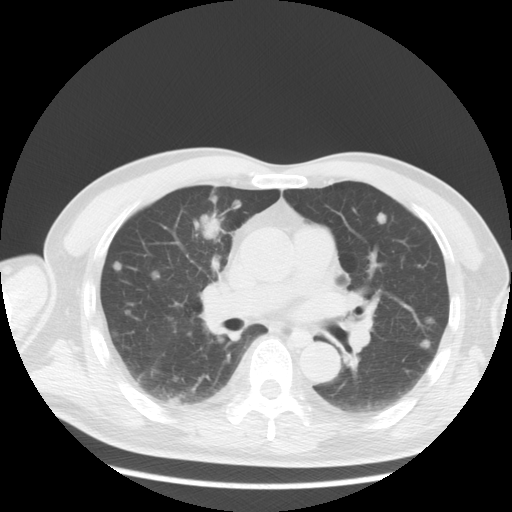
Chest CT, one axial slice; slice 10 of 36 in the series (ordered by position); reconstruction kernel STANDARD; 120 kVp; lung window (W 1500 / L -600 HU); 5 mm slice thickness; 512 × 512 image matrix, field of view 369 × 369 mm. Male patient, age 57 years. Case-level facts recorded for this patient, not image findings: clinical TNM (as recorded): T2 N3 M1a.
Structures marked on this image (rectangle marked by the reading radiologist):
- lung tumour (recorded histology: adenocarcinoma): bounding box [x1, y1, x2, y2] px = [204, 215, 220, 241]